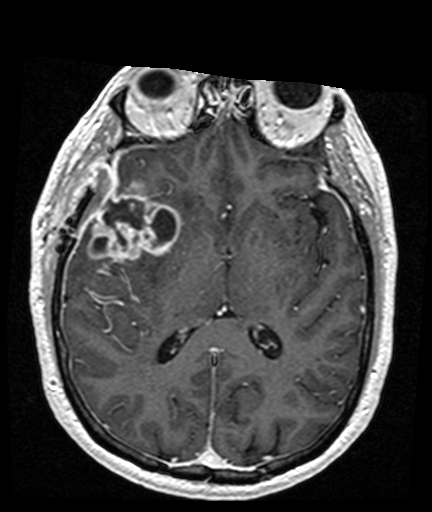
Brain MRI from a brain-tumour surgery series, one axial slice; position 83 of 176 along the scan axis; T1-weighted post-contrast; 432 × 512 image matrix. From the clinical record (not read from this slice): histopathology: Glioblastoma; WHO grade: 4; IDH mutation: no; tumour location: Right Frontal Temporal, Posterior Sylvian Fissure.
Outlined on this slice (manually delineated by an expert):
- tumour: bounding box [x1, y1, x2, y2] px = [86, 181, 181, 265]